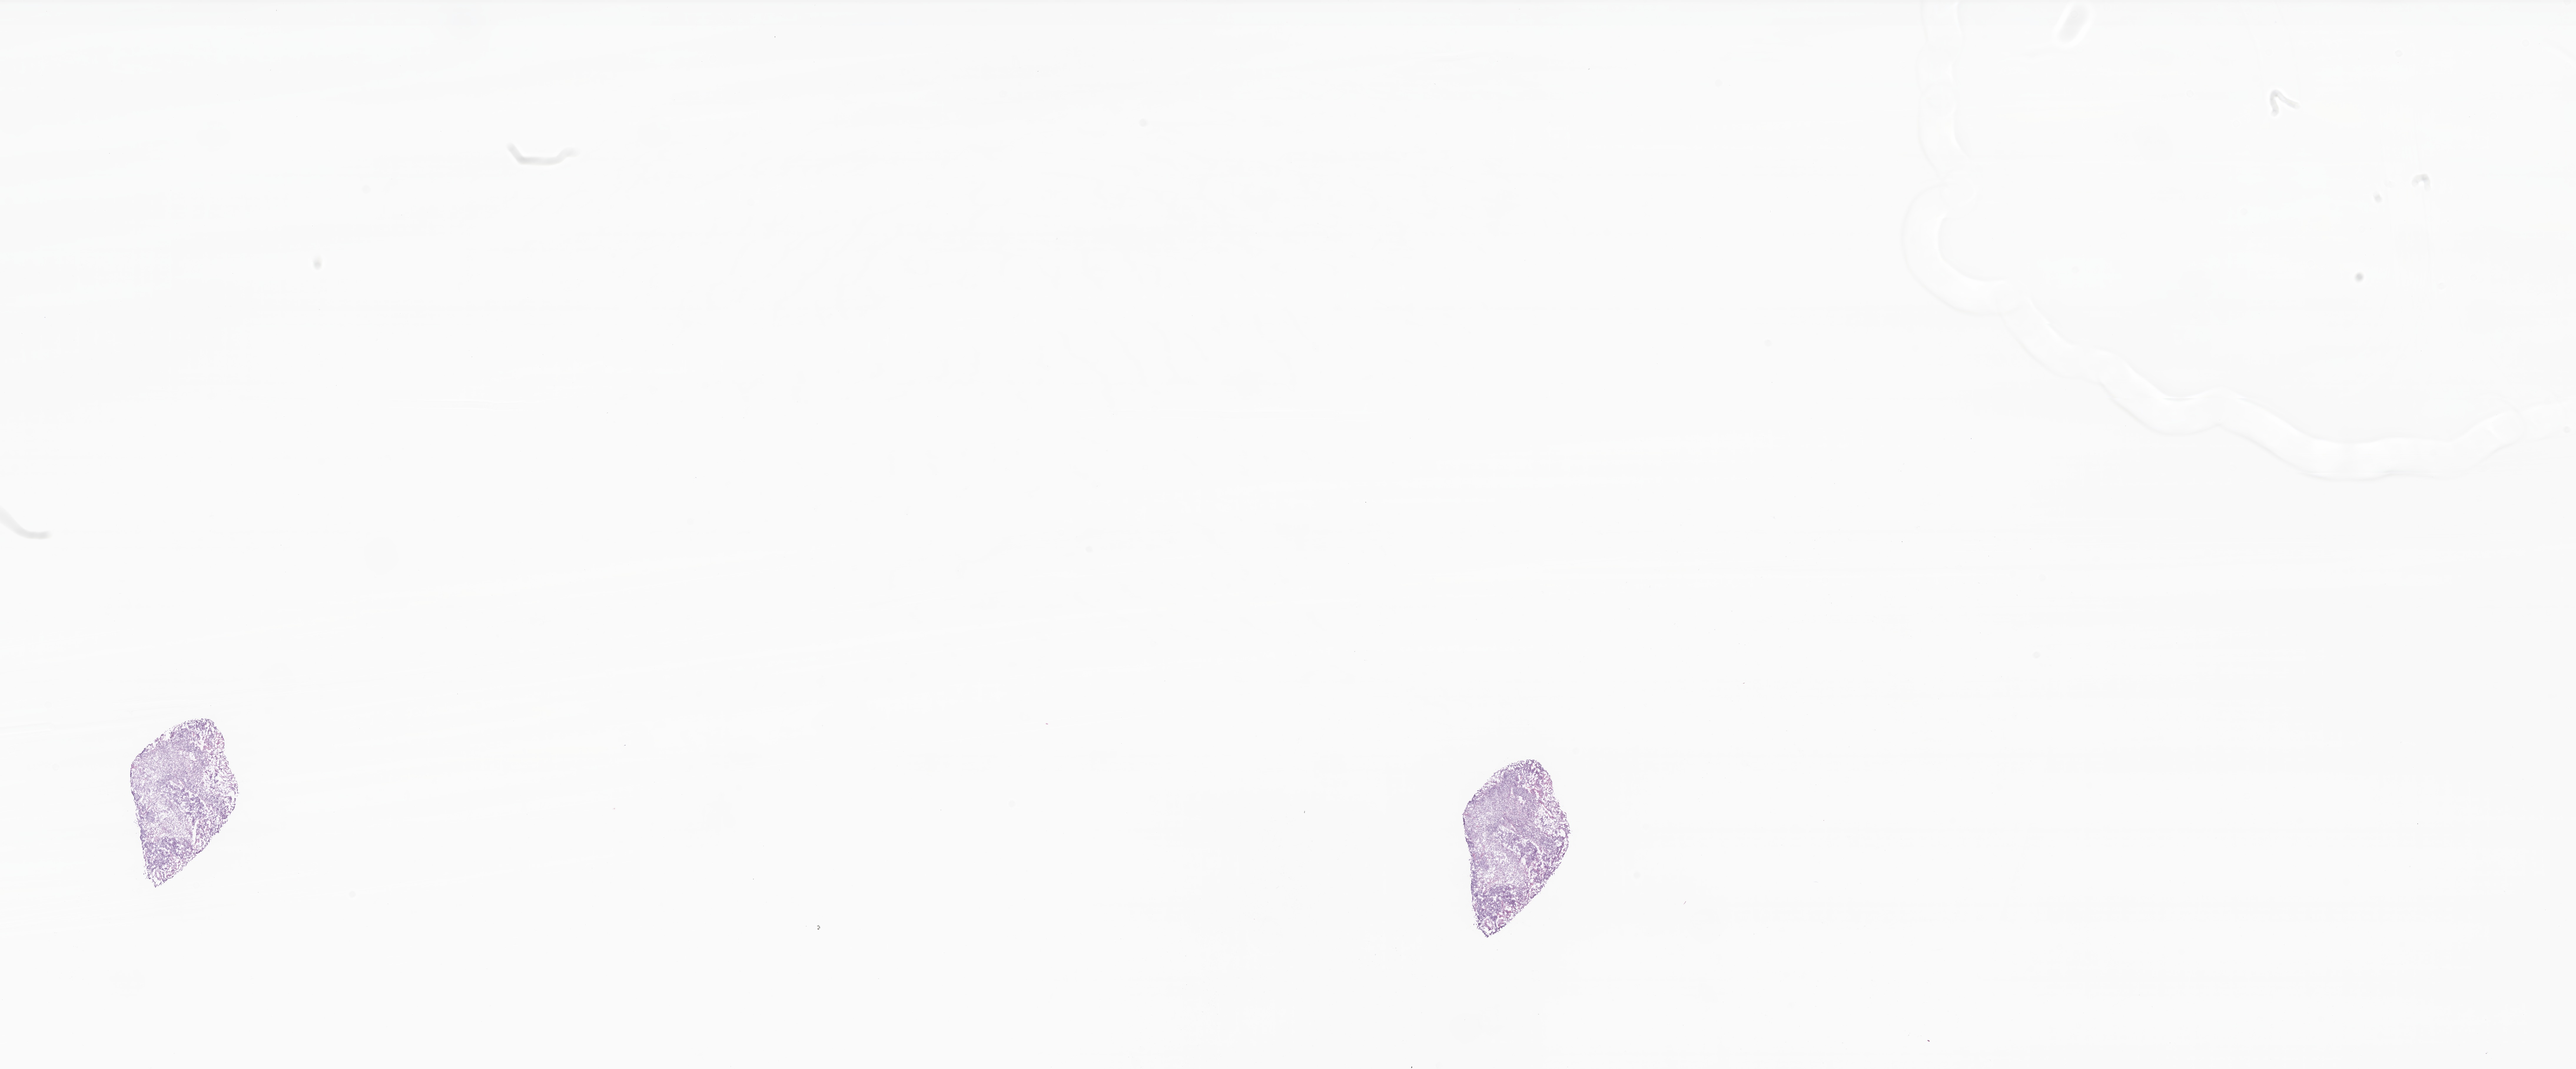
Digitized haematoxylin and eosin-stained section — low-resolution overview of the scanned area, about 36.9 x 15.3 mm; frozen section (tissue freezing medium); specimen: primary tumor; site: breast (right). Female patient; age at initial diagnosis 62 years. Pathologist review of this section (percent, as recorded): tumor cells 70%, tumor nuclei 90%, stromal cells 20%, necrosis 10%, normal cells 0%. Inflammatory infiltration, as recorded: lymphocyte infiltration 0%, monocyte infiltration 0%, neutrophil infiltration 0%.
- diagnosis: Infiltrating duct carcinoma, NOS